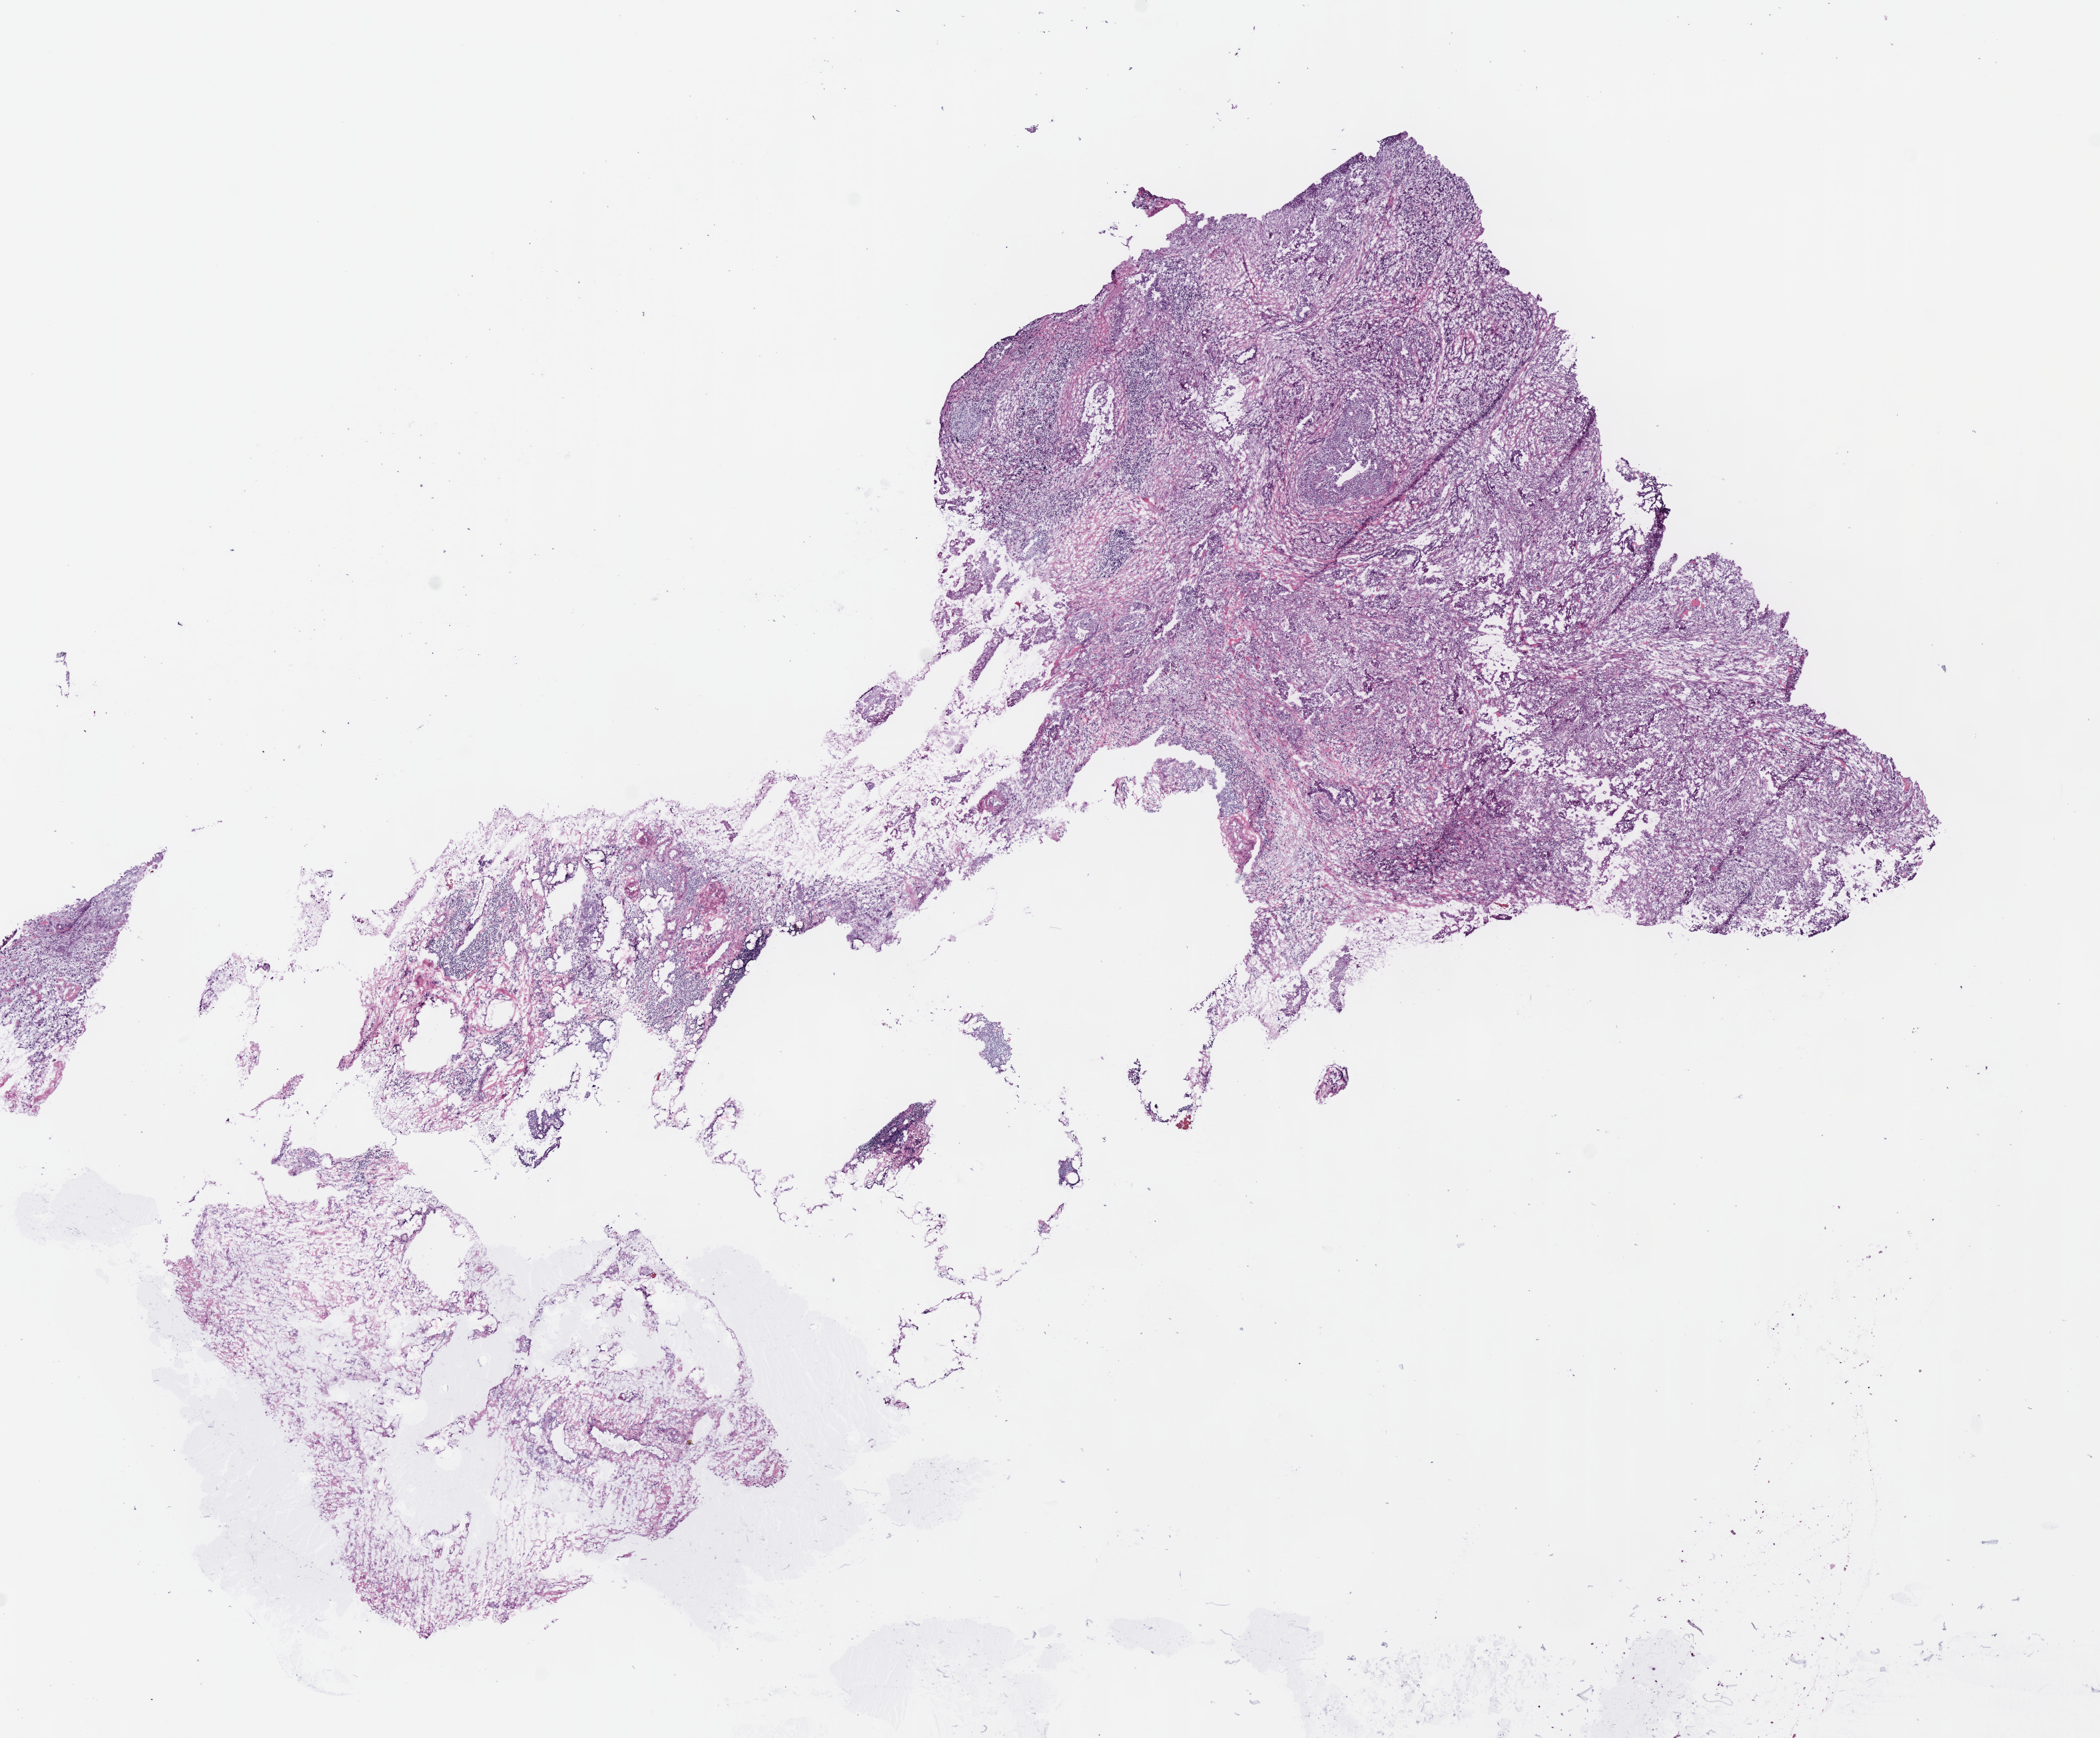
H&E-stained whole-slide image — low-resolution overview of the scanned area, about 12.4 x 10.3 mm. Frozen section from the bottom of the tissue portion. Pancreas, primary tumour sample. Patient: female, age at initial diagnosis 78 years. Histologic grade: G2 (moderately differentiated). Pathologist review of this section (percent, as recorded): tumour cells 60%, tumour nuclei 50%, normal cells 0%, stromal cells 40%, necrosis 0%.
Histologic diagnosis: Infiltrating duct carcinoma, NOS. AJCC pathologic stage: IIB (7th edition).